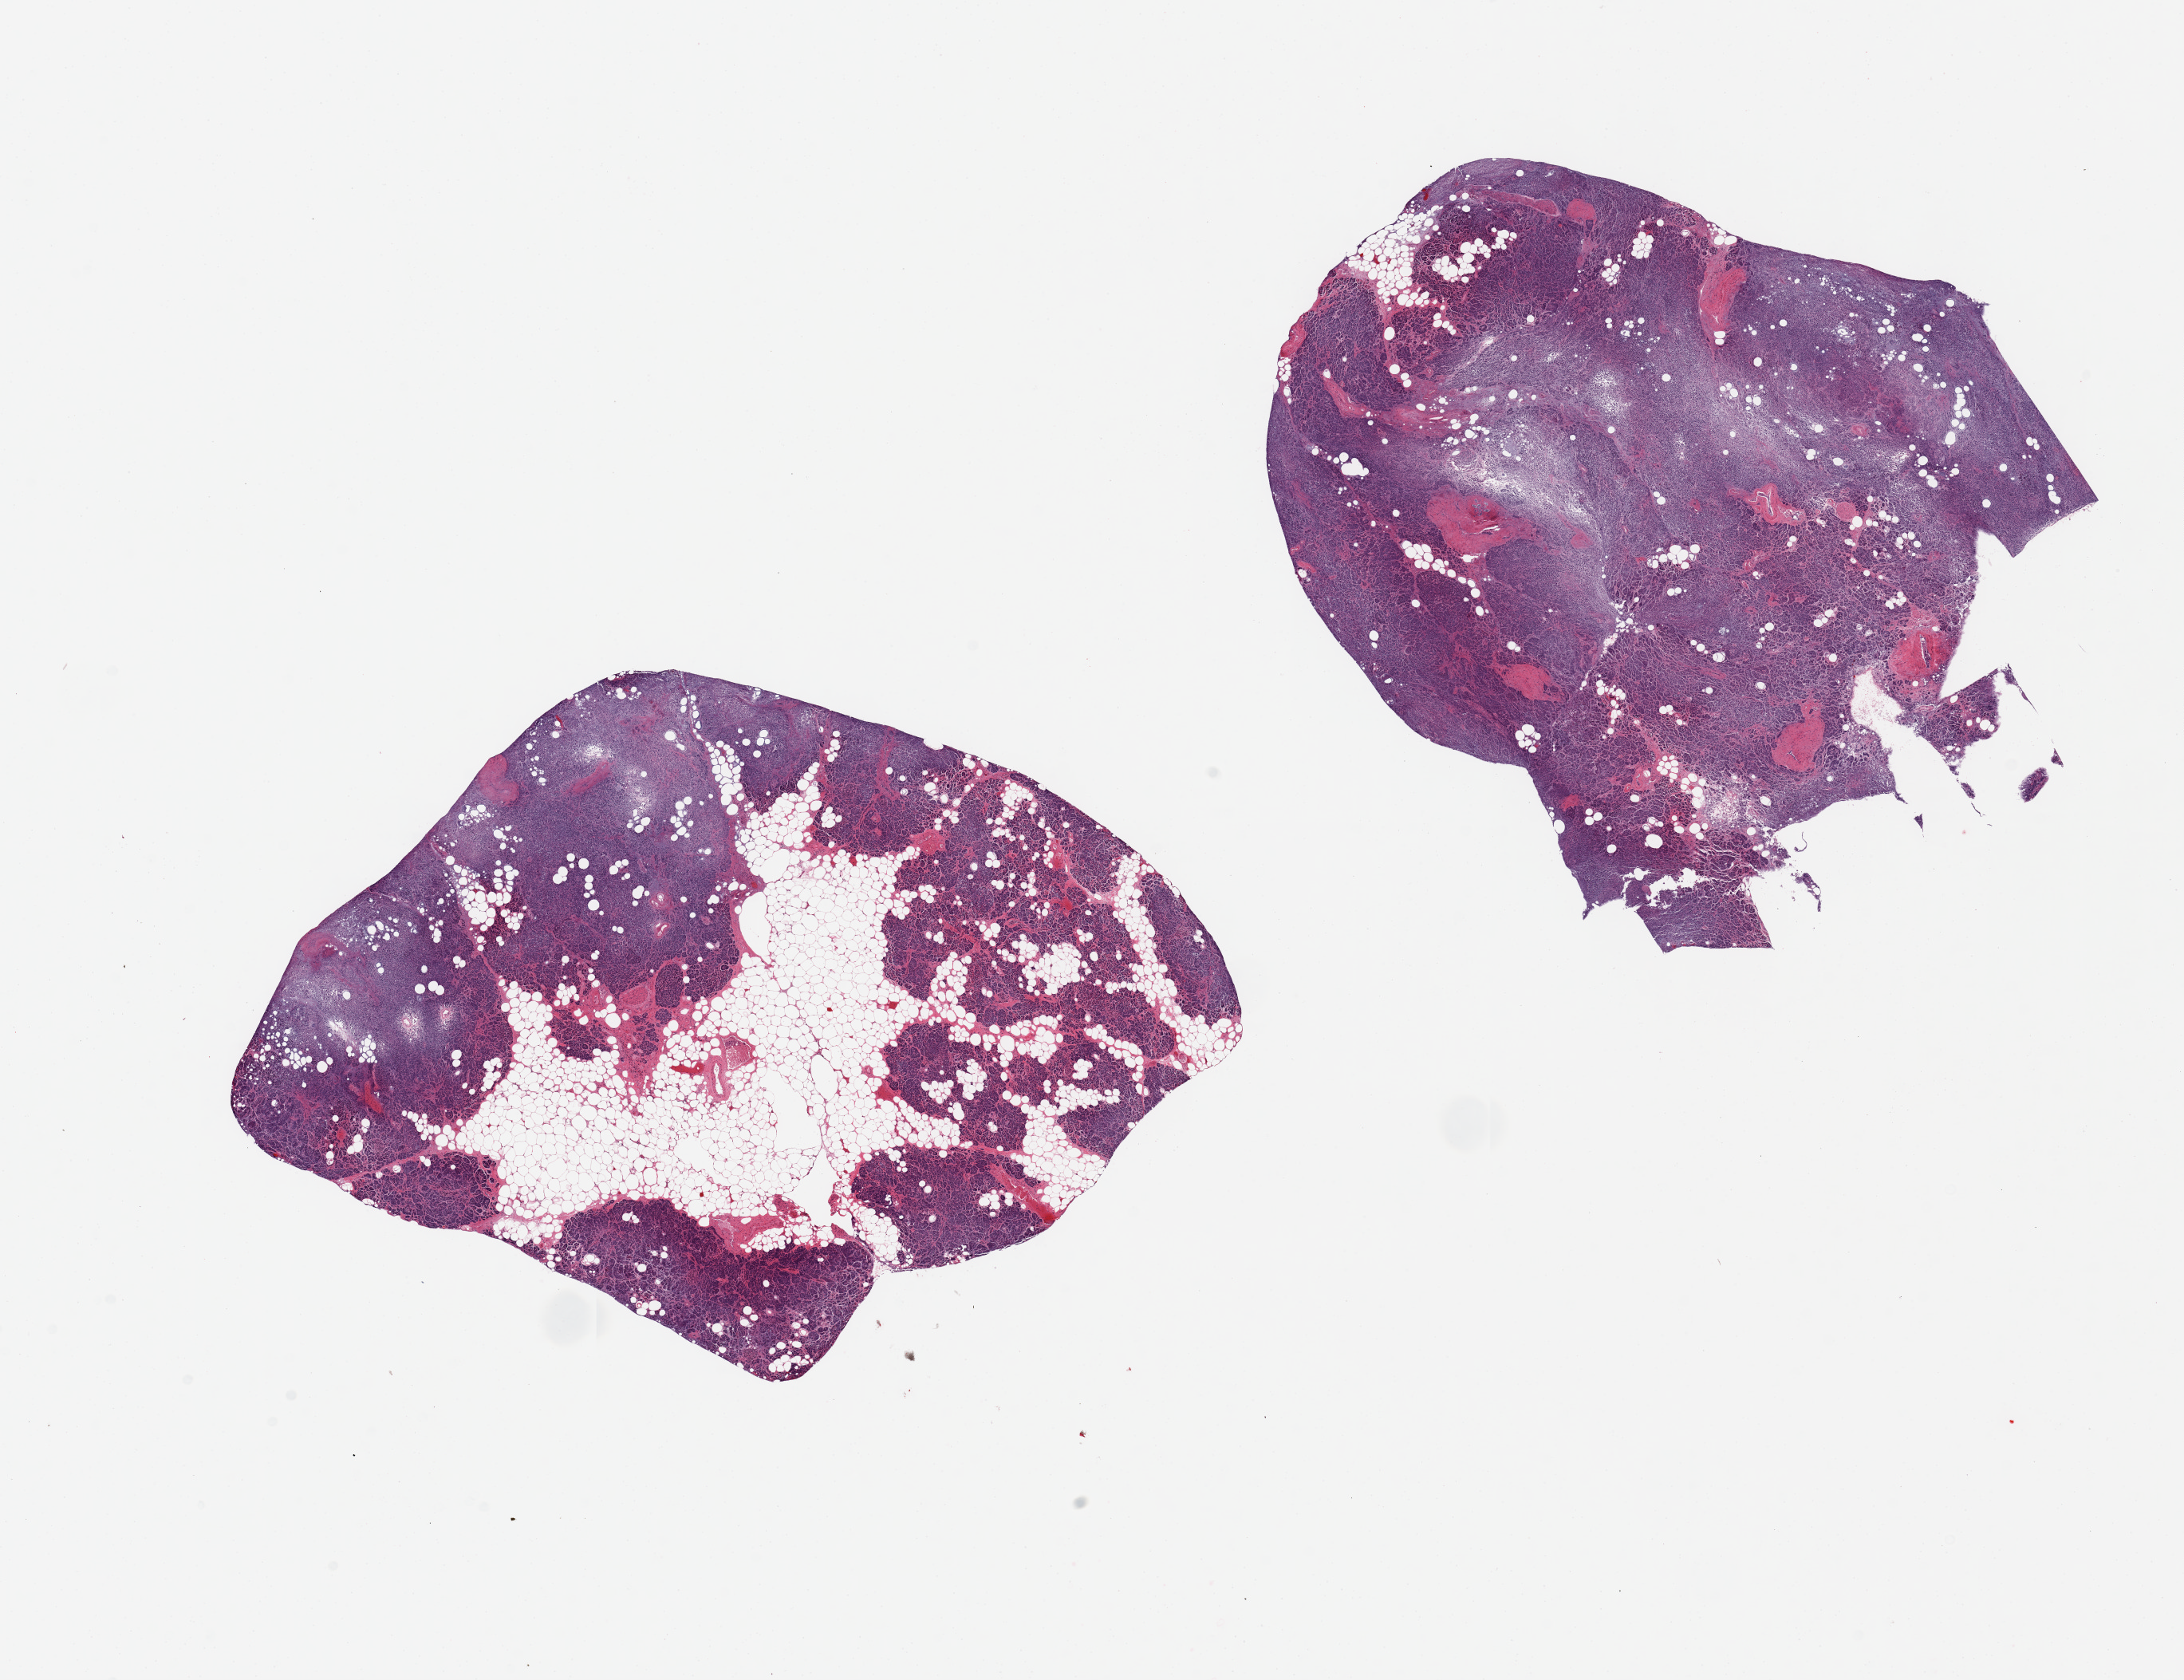
Whole-slide image, haematoxylin and eosin stain — whole scanned area (about 21.7 x 16.7 mm) shown as a low-resolution overview, PAXgene-fixed paraffin-embedded (PFPE) section, section of pancreas (target tissue), tissue donor sample. Donor sex: male.
* review note (as recorded): 2 pieces; one piece is 30% fat, moderate to severe autolysis